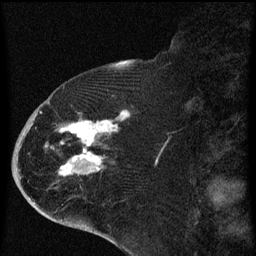
Breast MRI (dynamic contrast-enhanced), one sagittal slice; position 26 of 60 along the scan axis; dynamic contrast-enhanced series, image 2 of 4 at this slice position (ordered by acquisition); 1.5 T; TE 4.2 ms, TR 8 ms; 256 × 256 image matrix. Patient: female, 71 years.
Outlined on this slice (semi-automatic segmentation, software-assisted and operator-edited):
- analysis volume of interest (the breast-tissue region the enhancement analysis was run in; not a lesion): bounding box (x1, y1, x2, y2) in pixels: (32, 86, 140, 205)
- tumour enhancement mask (voxels above the 70 % enhancement threshold inside the analysis volume of interest): (40, 110, 130, 177)